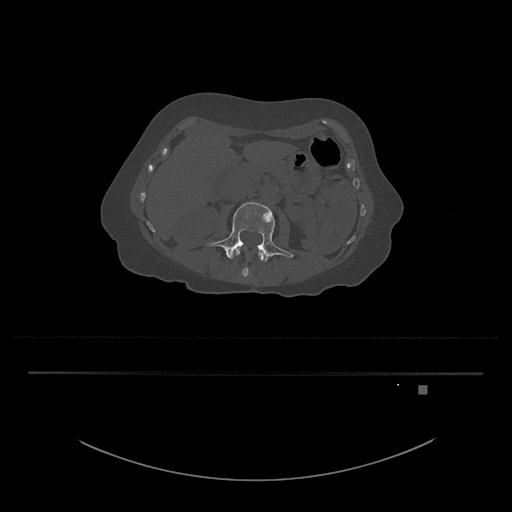
CT including the spine, one axial slice; slice 441 of 797 in the series (ordered by position); 120 kVp; bone window (W 1800 / L 400 HU); 512 × 512 image matrix, field of view 500 × 500 mm. Patient: female, 57 years. Case-level facts recorded for this patient, not image findings: primary cancer: cervical.
Outlined on this slice (semi-automatic segmentation, software-assisted and operator-edited):
- L3 vertebra: bounding box [x1, y1, x2, y2] px = [207, 202, 293, 262]